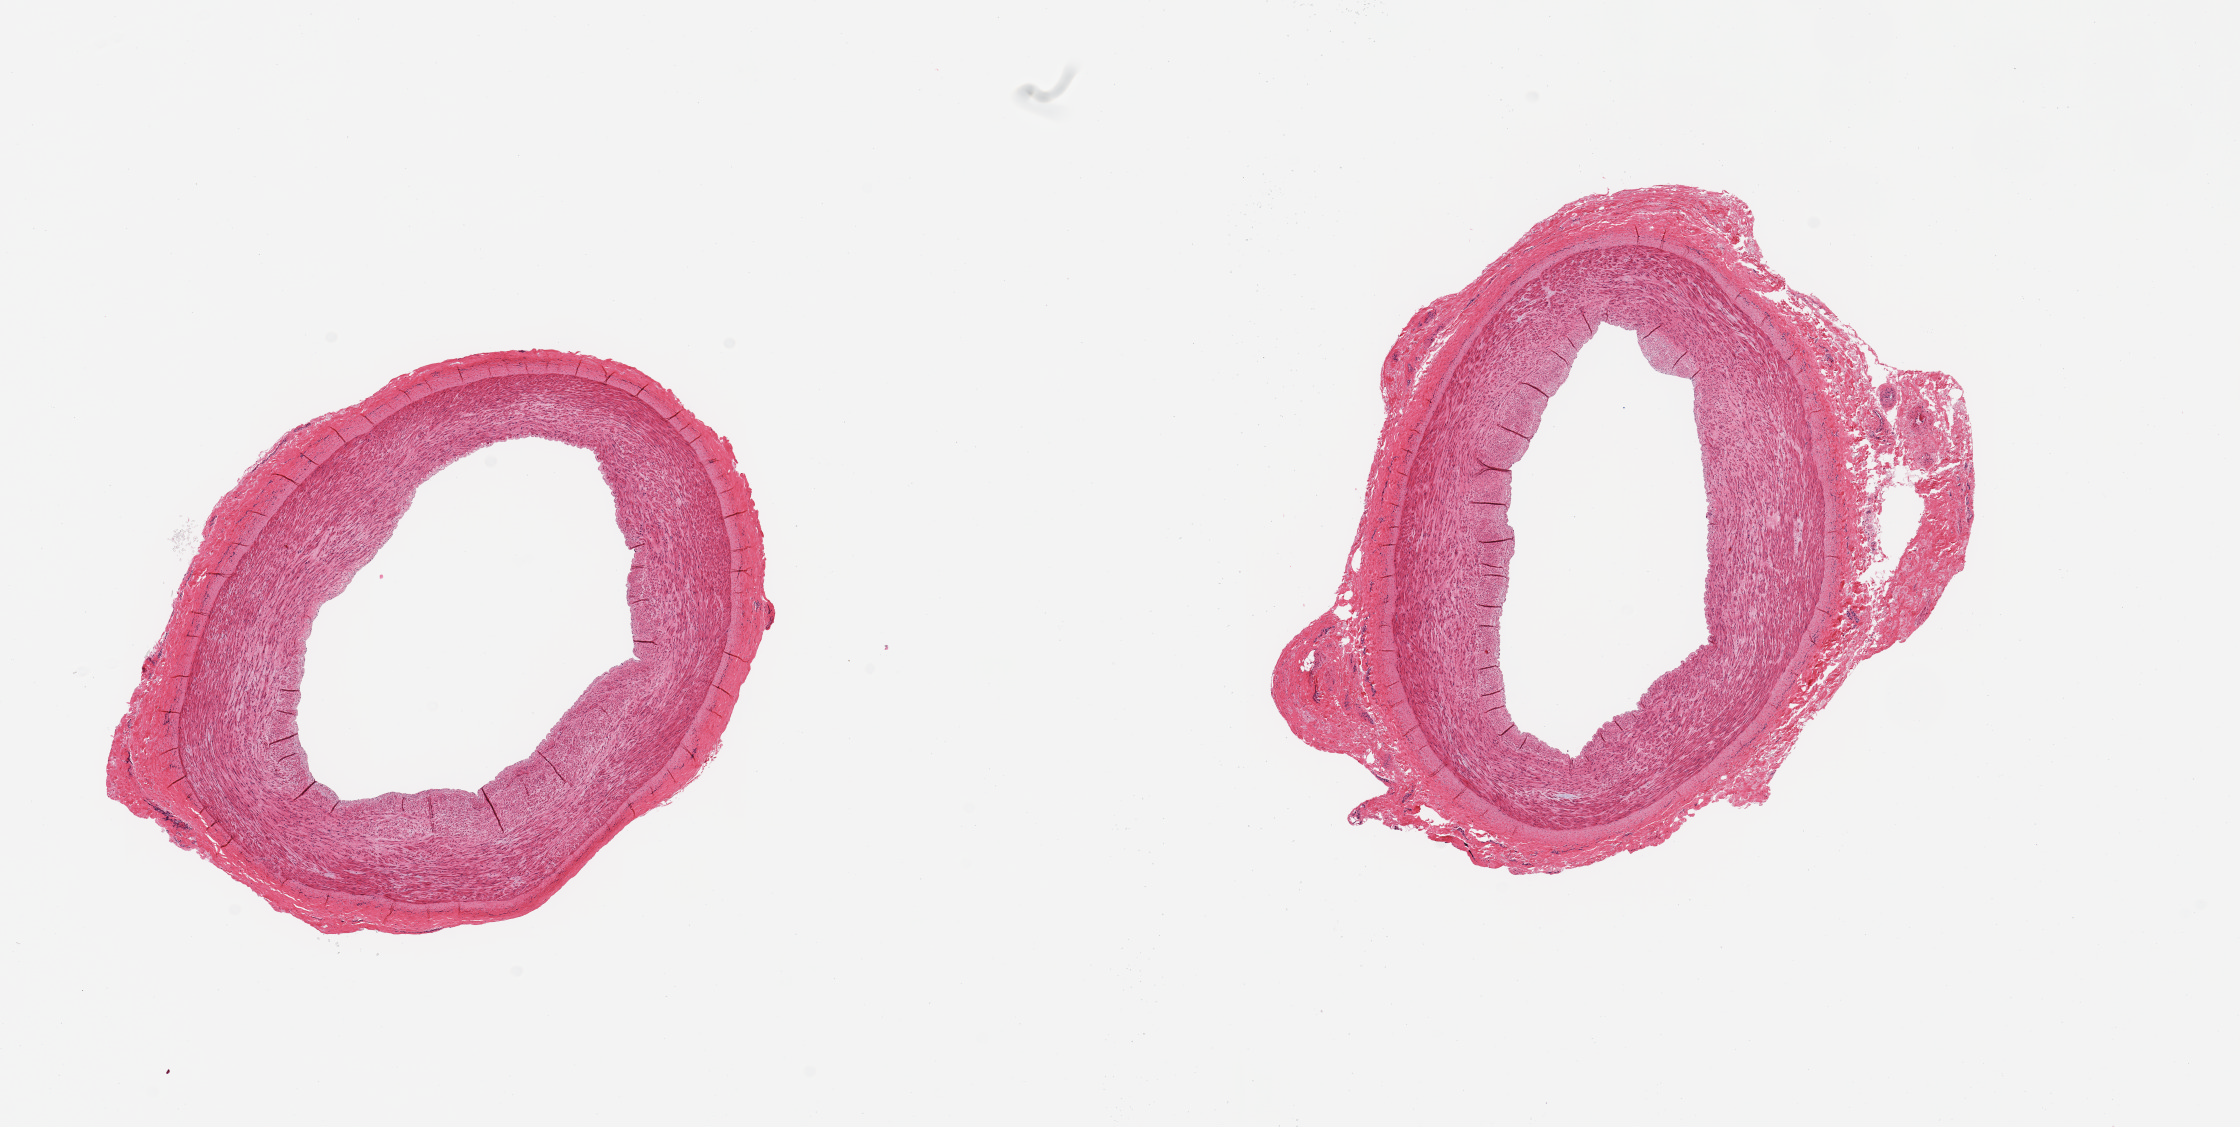
Haematoxylin and eosin whole-slide image, low-resolution overview of the scanned area, about 17.7 x 8.9 mm (acquisition: 20x scan), PAXgene-fixed, paraffin-embedded tissue, sampled site (target tissue): tibial nerve, donor tissue sample. Donor: male.
Pathologist's review note for this sample: 2 pieces, muscular artery, no neural tissue is present.